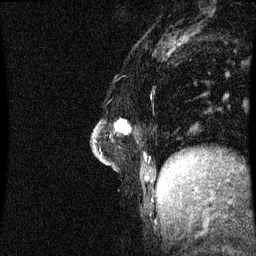
Breast MRI (dynamic contrast-enhanced), one sagittal slice; slice 15 of 60 in the series (ordered by position); dynamic contrast-enhanced series, image 2 of 3 at this slice position (ordered by acquisition); 1.5 T; TE 4.2 ms, TR 8.9 ms; 256 × 256 image matrix, field of view 200 × 200 mm. Female patient, age 47 years. Case-level facts recorded for this patient, not image findings: setting: breast cancer imaged before/during neoadjuvant chemotherapy; receptor status: HR-positive, HER2-negative.
Outlined on this slice (semi-automatic segmentation, software-assisted and operator-edited):
- analysis volume of interest (the breast-tissue region the enhancement analysis was run in; not a lesion): bounding box <94,124,126,163> (left, top, right, bottom; pixels)
- tumour enhancement mask (voxels above the 70 % enhancement threshold inside the analysis volume of interest): <117,124,125,131>